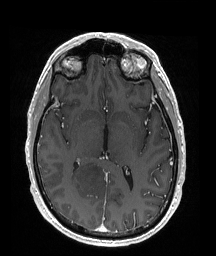
Brain MRI from a brain-tumour surgery series, one axial slice; position 97 of 176 along the scan axis; T1-weighted post-contrast; 1 mm slice thickness; 216 × 256 image matrix, field of view 211 × 250 mm. From the clinical record (not read from this slice): histopathology: Oligodendroglioma; WHO grade: 2; IDH mutation: yes.
Structures marked on this image (expert manual segmentation):
- tumour: bounding box <70,158,111,195> (left, top, right, bottom; pixels)